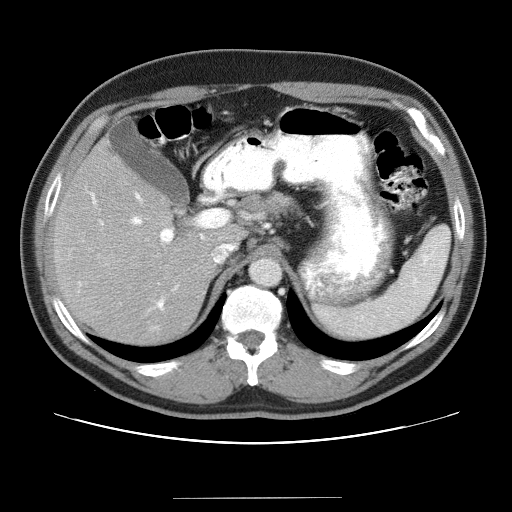
Contrast-enhanced abdominal CT (liver protocol), one axial slice; position 22 of 40 along the scan axis; reconstruction kernel STANDARD; soft-tissue window (W 400 / L 40 HU); 512 × 512 image matrix, field of view 380 × 380 mm. From the clinical record (not read from this slice): diagnosis: hepatocellular carcinoma (patient treated with transarterial chemoembolisation; whether this scan precedes or follows treatment is not stated here); TNM stage (as recorded): Stage-IVA; Child-Pugh class: B; tumour nodularity: multinodular.
Outlined on this slice (semi-automatic segmentation, software-assisted and operator-edited):
- liver parenchyma outside the tumour (the mass and vessels are separate outlines, so this box may not span the whole liver): box from (x=52, y=136) to (x=246, y=344) px
- liver vessels: (x=78, y=191)–(x=205, y=328)